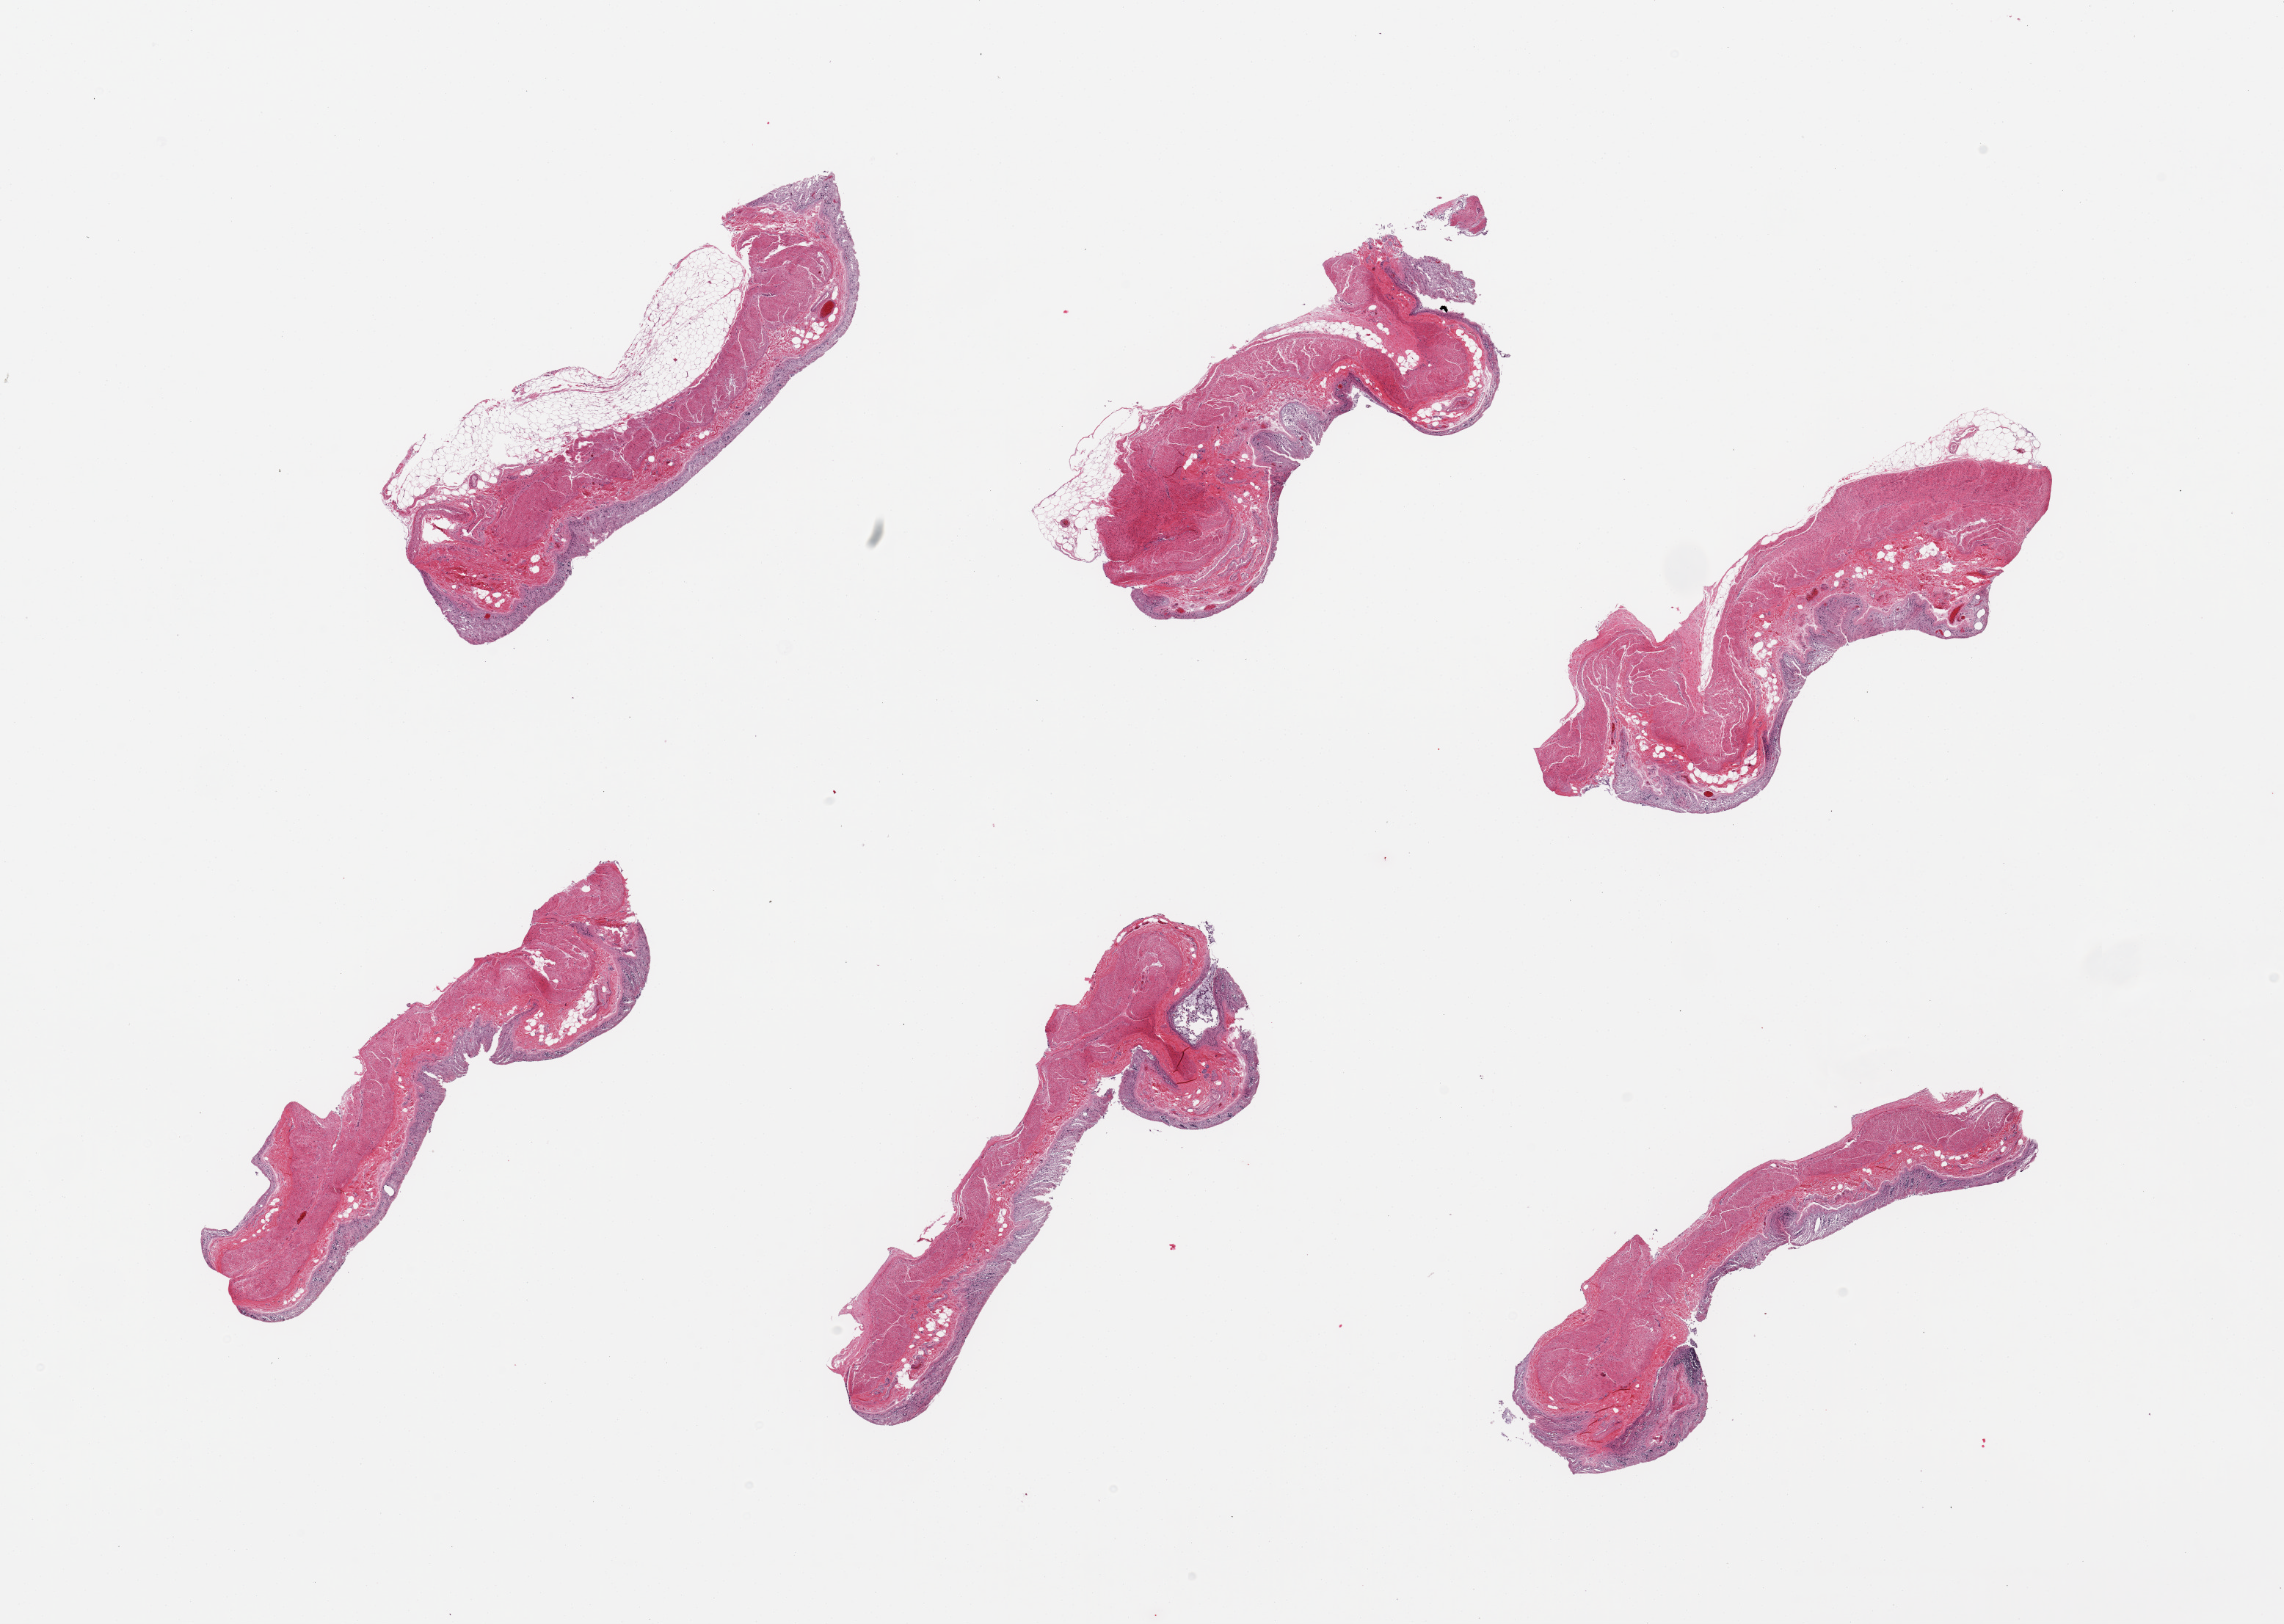
Hematoxylin and eosin (H&E) whole-slide image — low-resolution overview of the scanned area, about 24.6 x 17.5 mm (acquisition: 20x scan), PAXgene-fixed, paraffin-embedded tissue, section of transverse colon (target tissue), tissue donor sample. Donor: male.
- pathologist's review note for this sample: 6 pieces, target mucosa is totally autolyzed